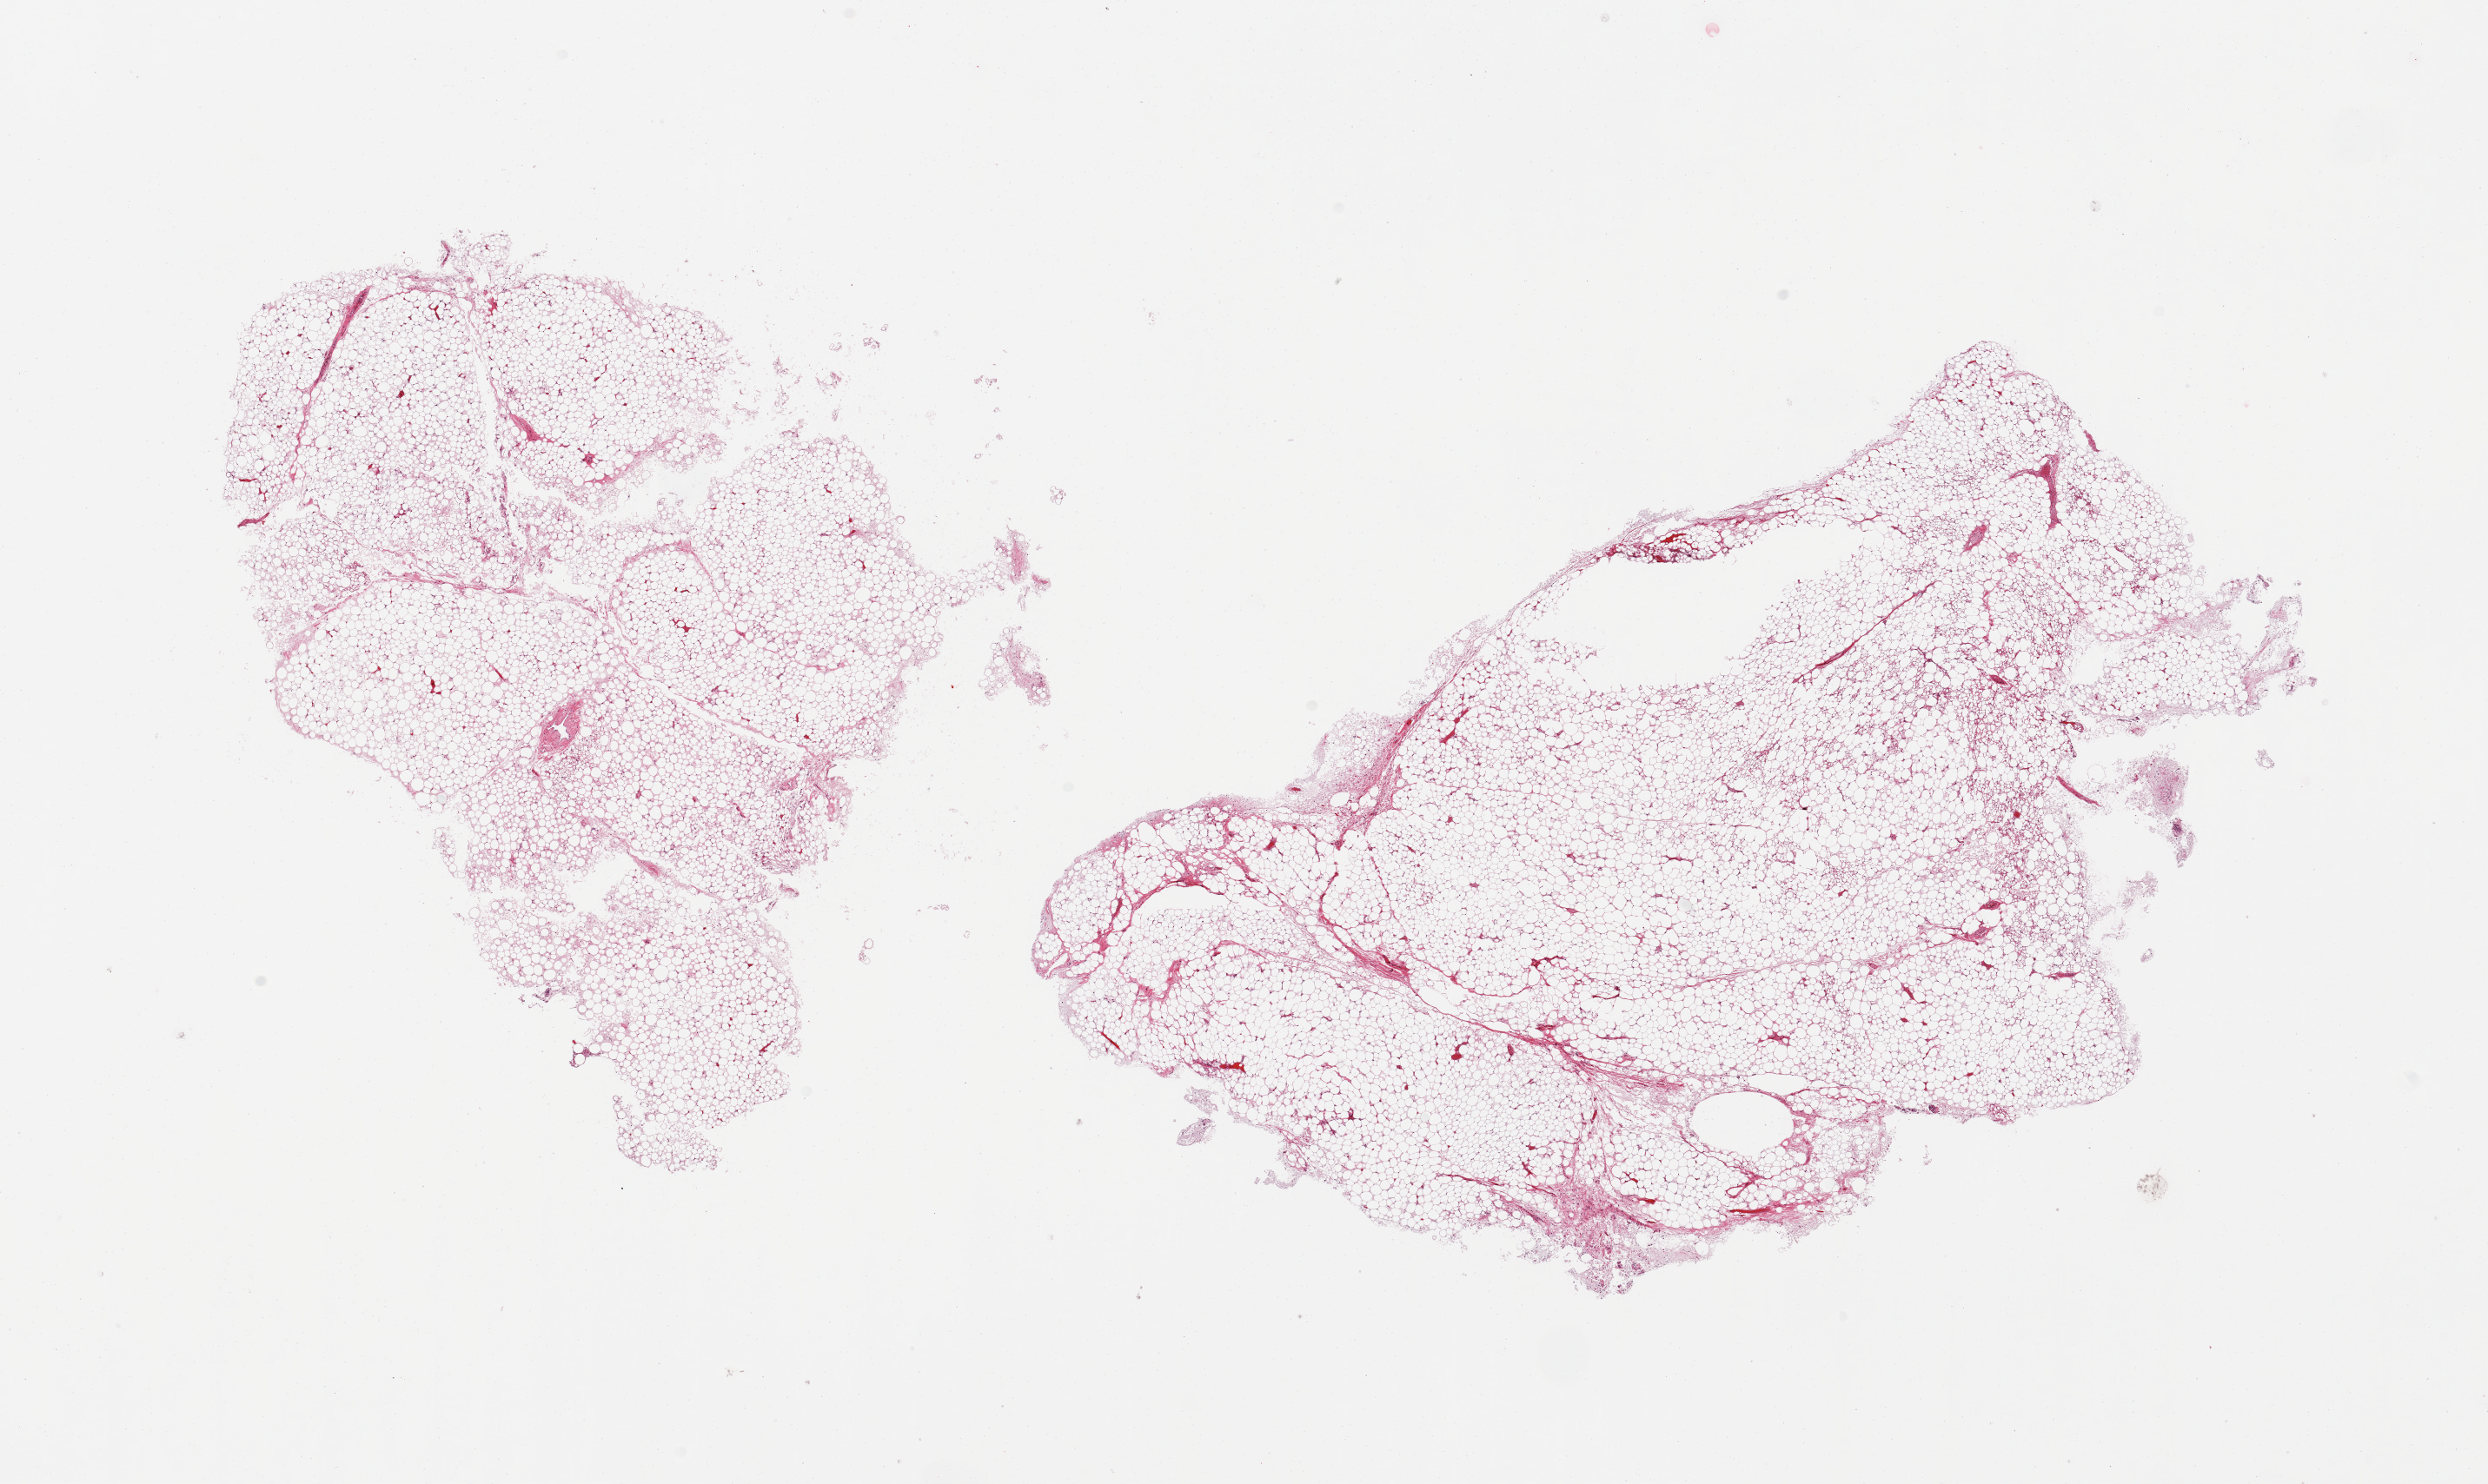
Whole-slide image, hematoxylin and eosin (H&E) stain, shown as a low-resolution overview of the whole scanned area (about 22.6 x 13.5 mm), PAXgene-fixed, paraffin-embedded tissue, target tissue: adrenal gland, tissue donor sample. Male donor.
* pathologist's review note for this sample: 2 pieces; fat only